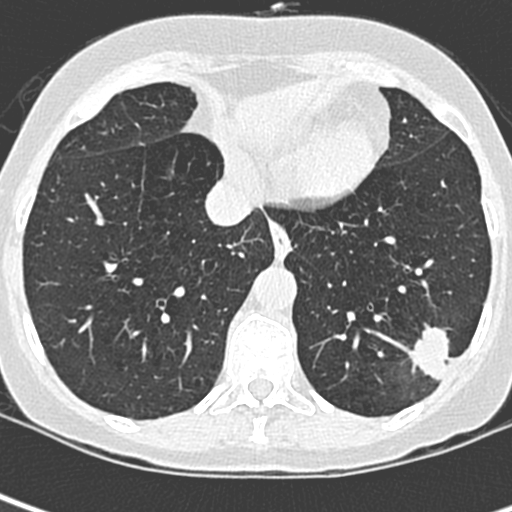
Low-dose screening chest CT, one axial slice; slice 85 of 252 in the series (ordered by position); 120 kVp; lung window (W 1500 / L -600 HU); 1.3 mm slice thickness; 512 × 512 image matrix, field of view 271 × 271 mm.
Structures marked on this image (expert manual segmentation):
- lesion 1 (tumor, lower lobe of left lung): bounding box (x1, y1, x2, y2) in pixels: (408, 327, 456, 381)